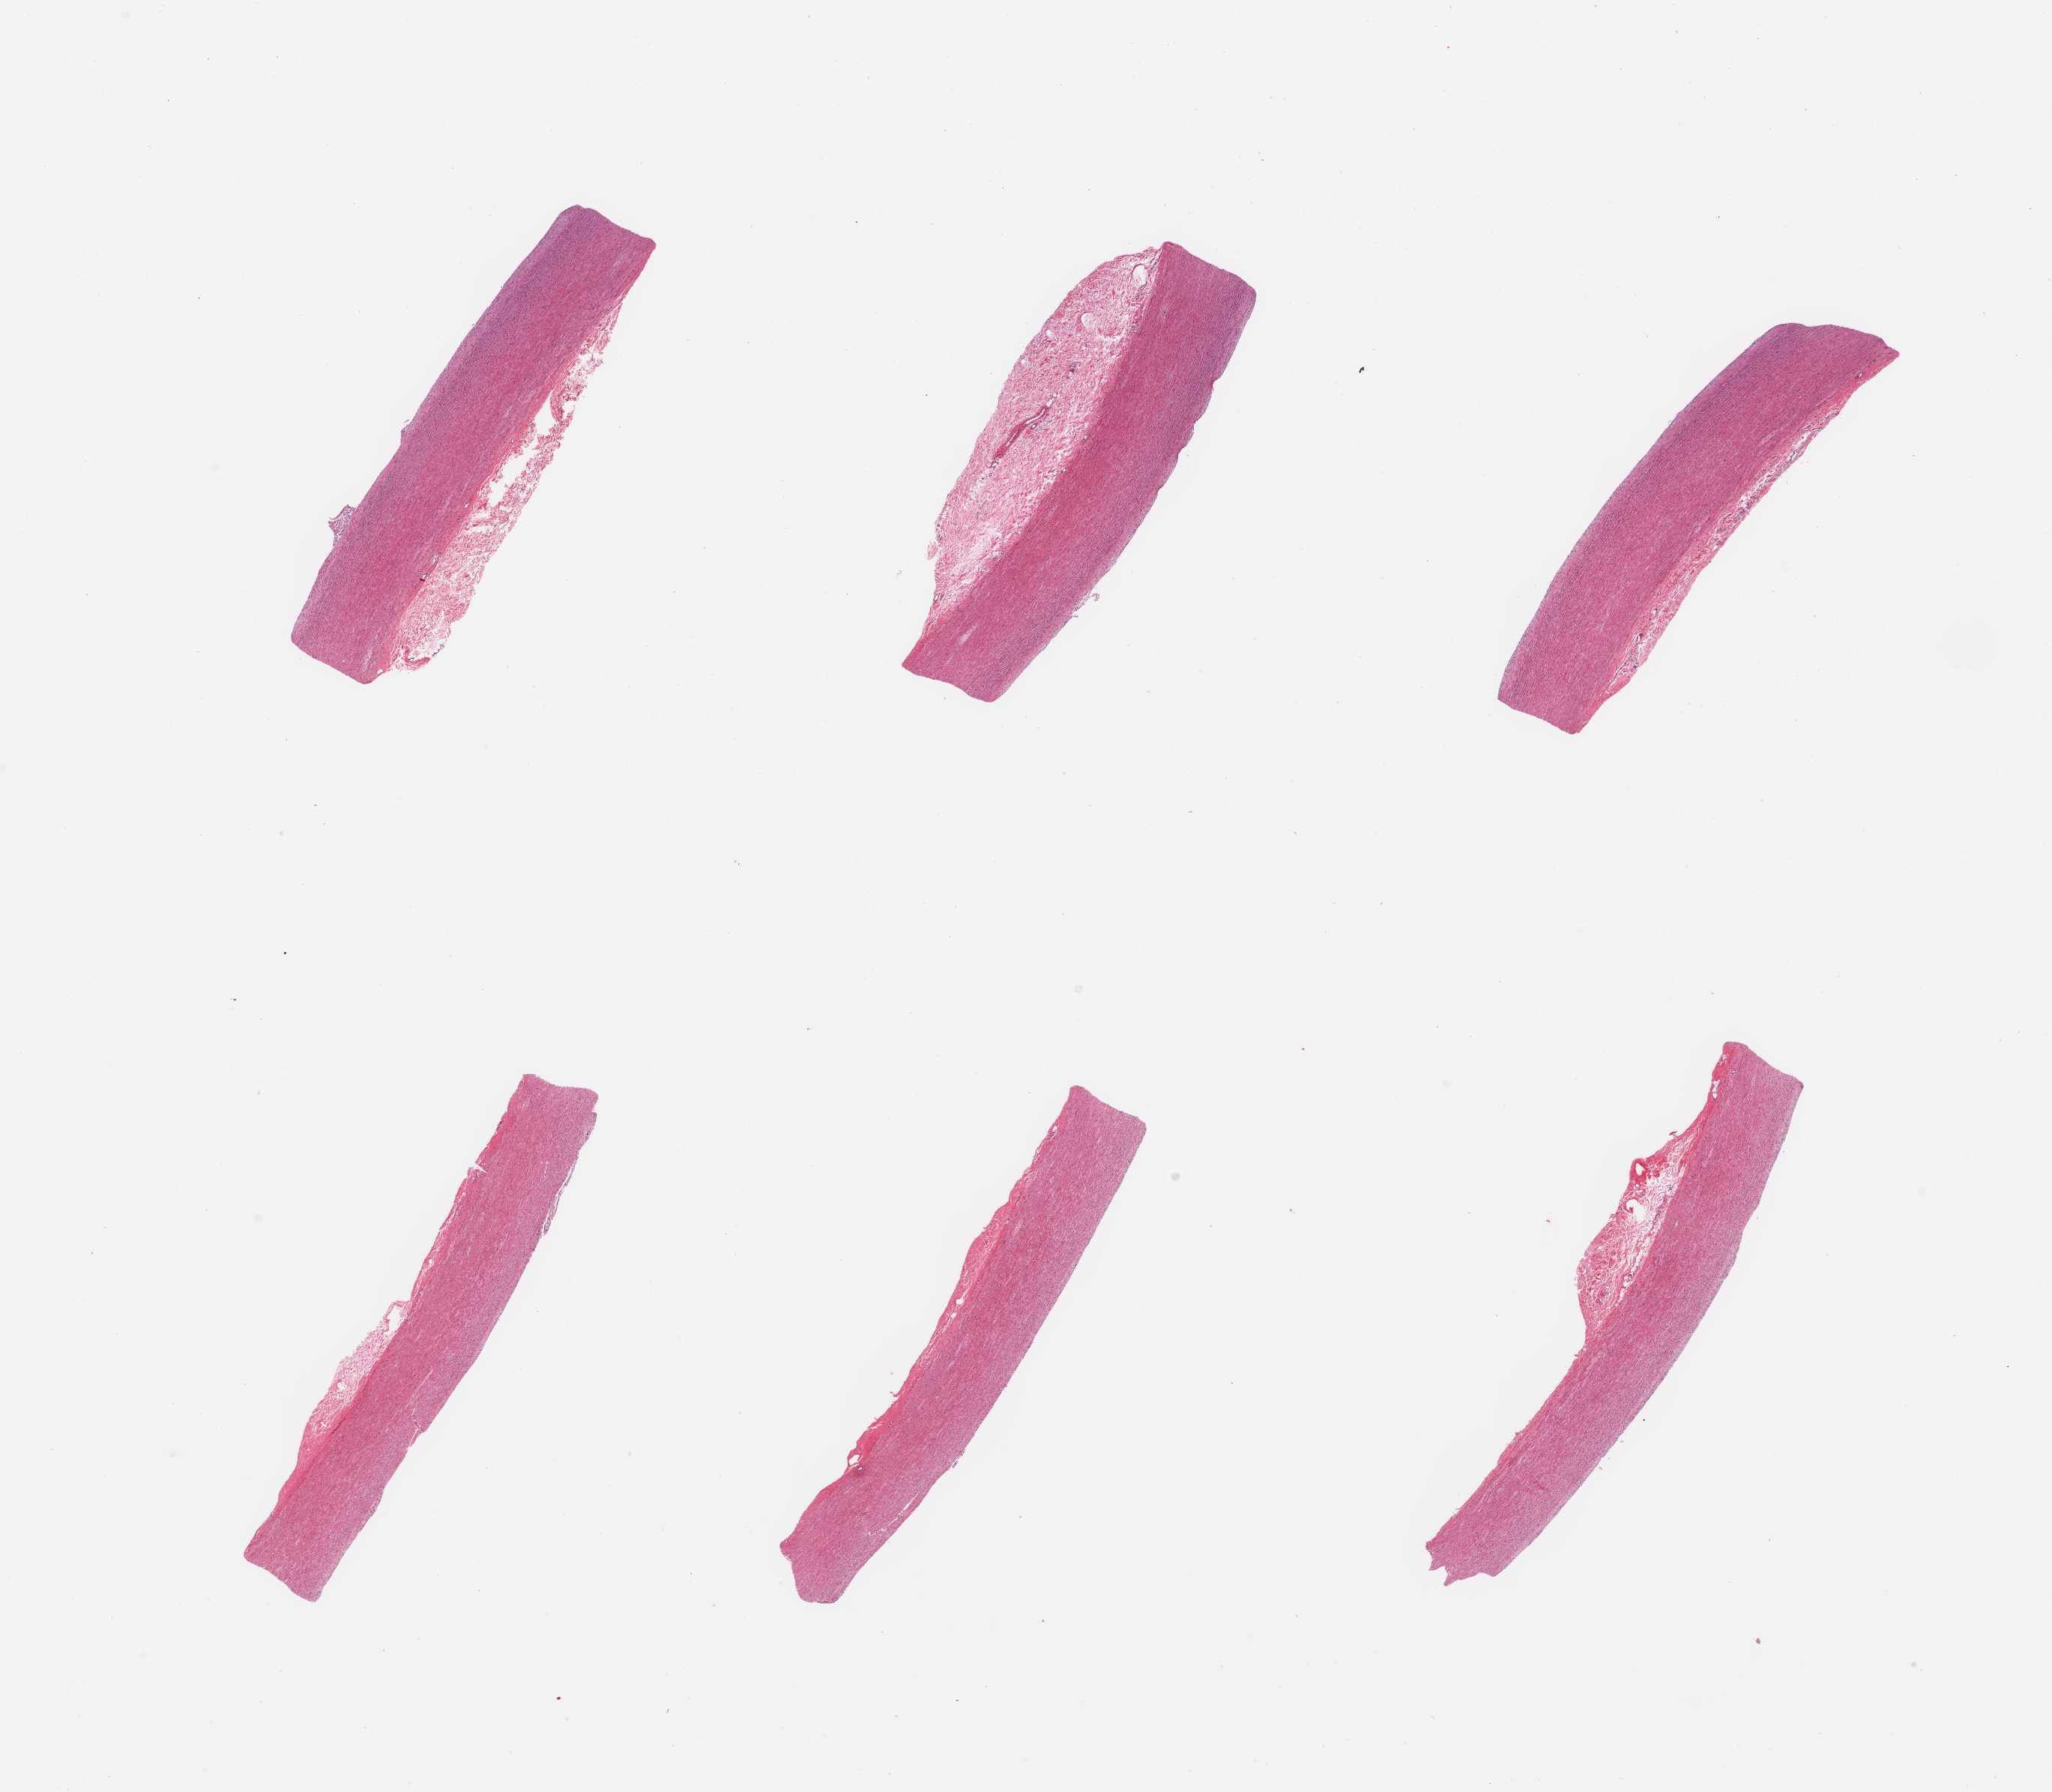
Digitized hematoxylin and eosin (H&E)-stained section, brightfield — a low-resolution overview of the entire scanned area, about 21.7 x 18.9 mm (acquisition: 20x scan), PAXgene-fixed paraffin-embedded (PFPE) section, target tissue: aorta, donor tissue sample. Male donor.
Pathologist's review note for this sample: 6 pieces; no plaques; fibrous adventitia up to 1mm thick.